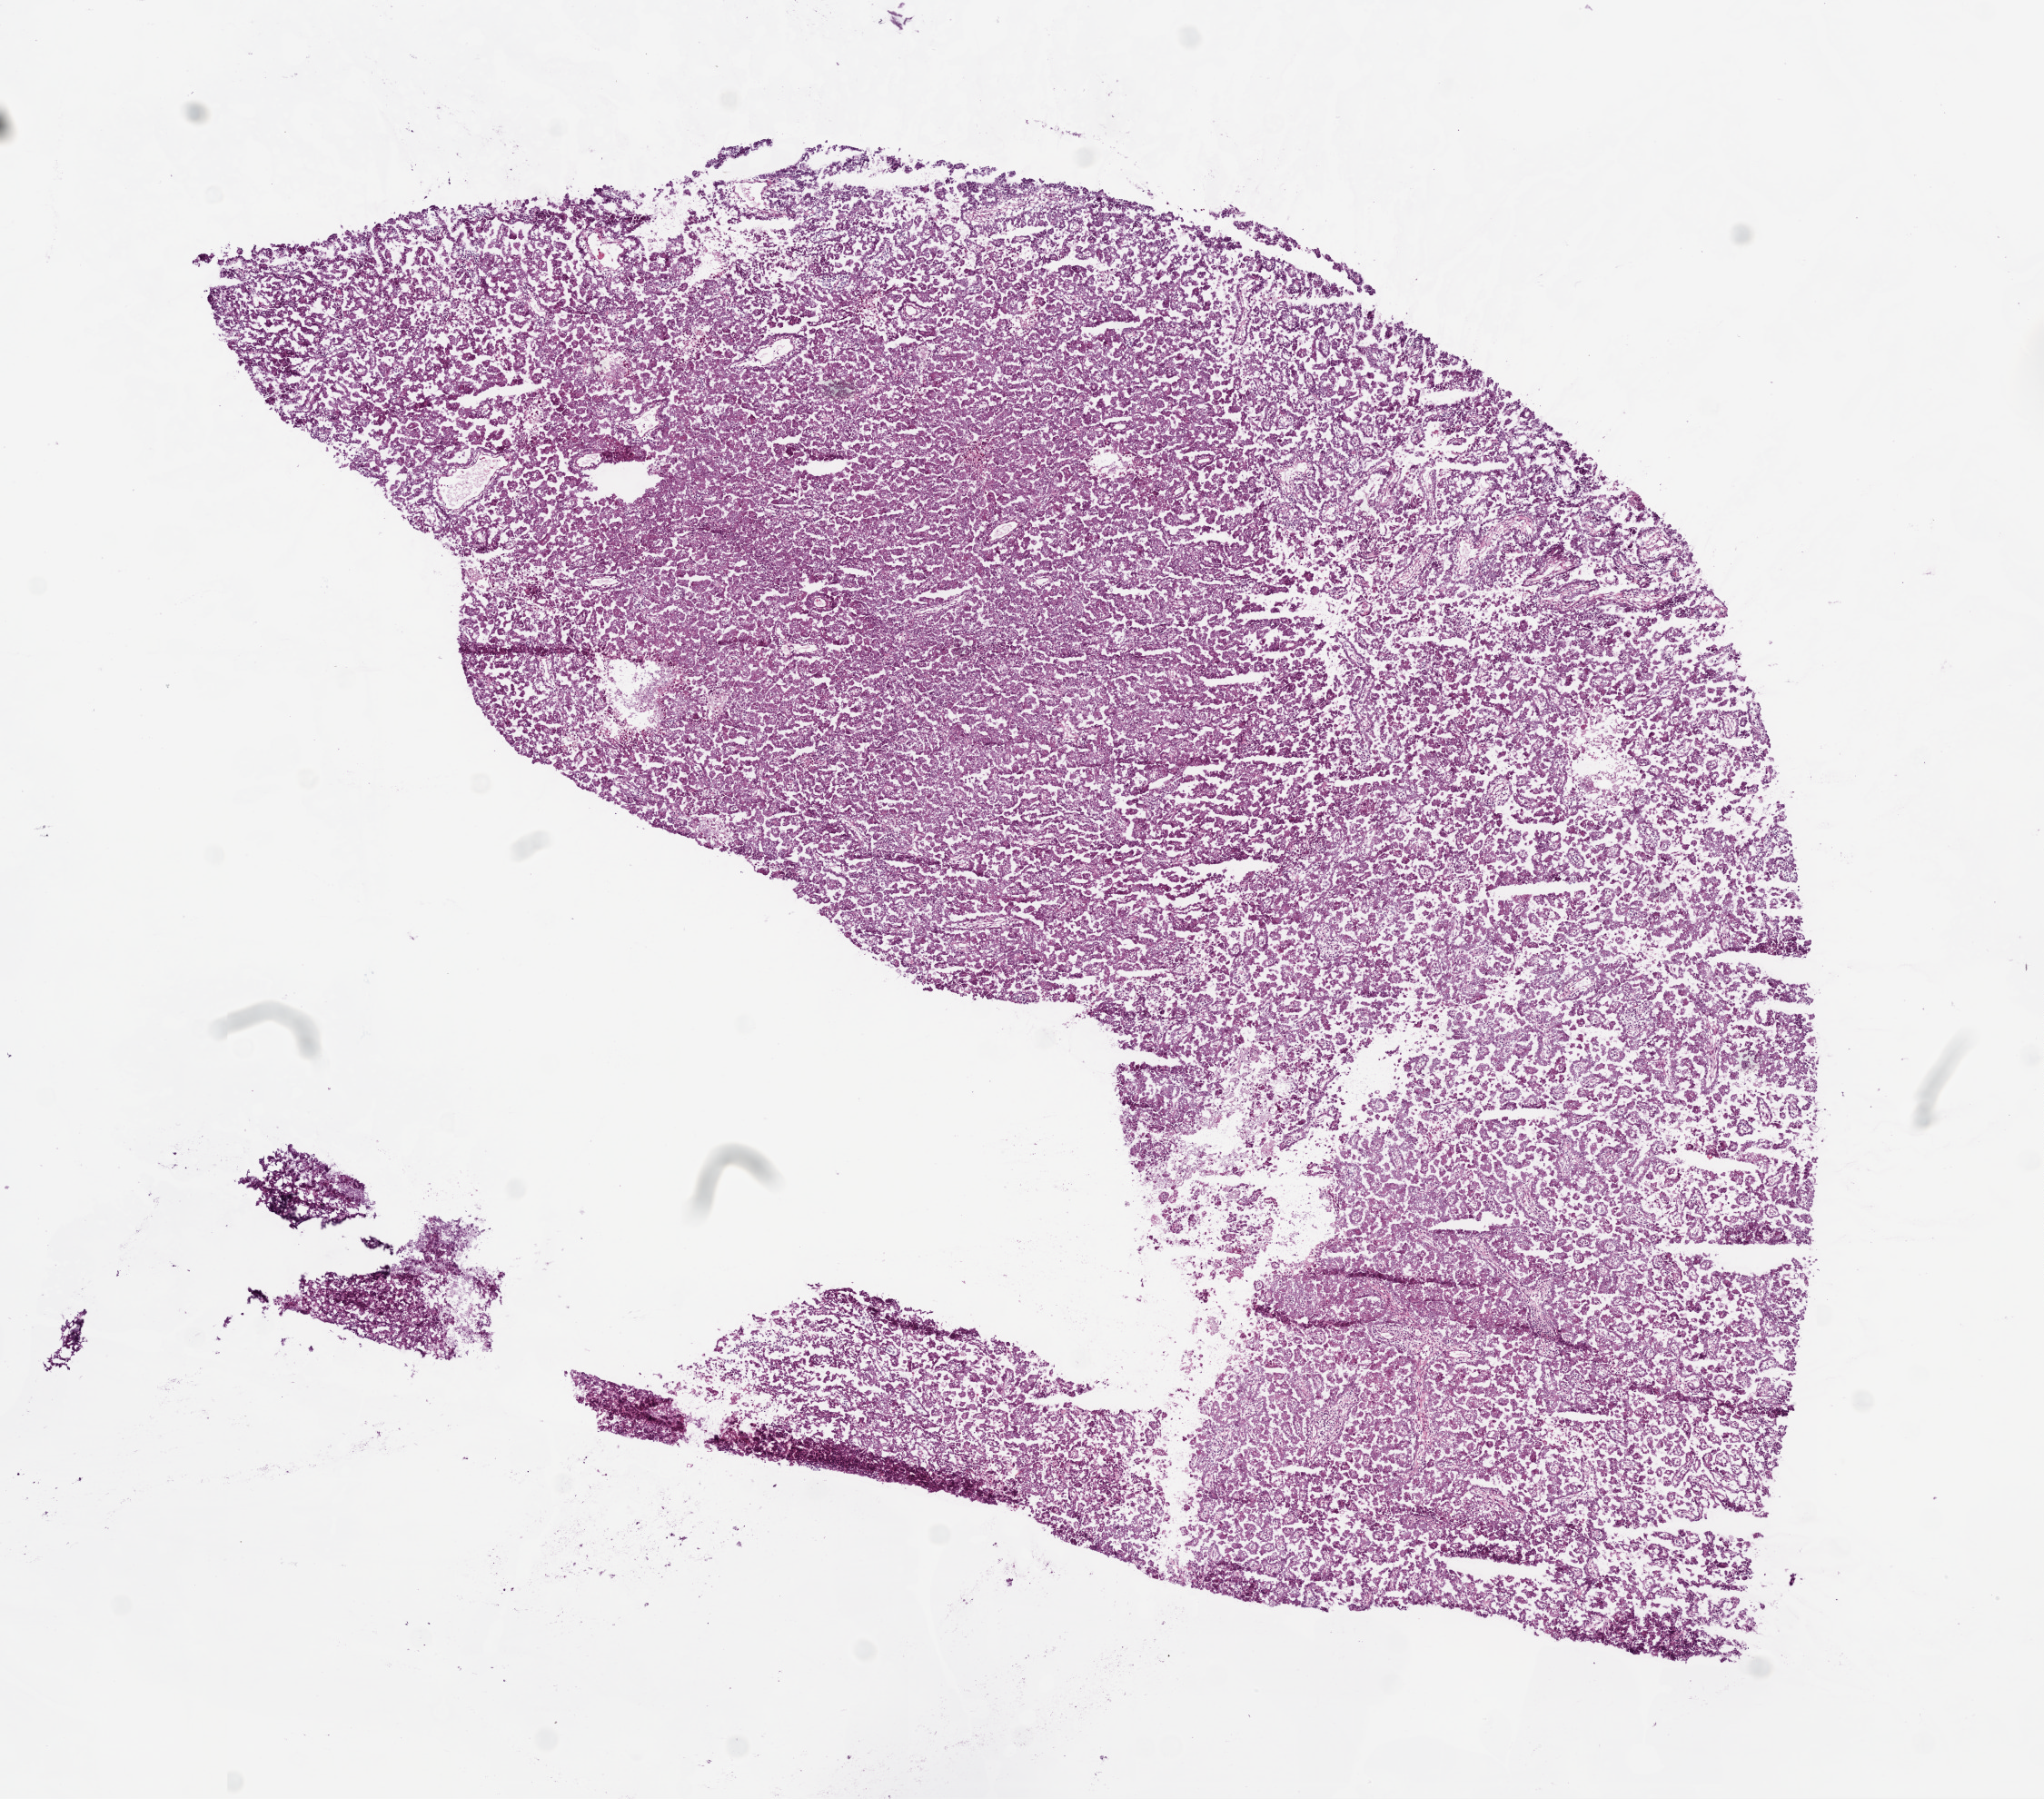
H&E-stained whole-slide image, whole scanned area (about 9.0 x 7.9 mm, acquisition: 20x scan) shown as a low-resolution overview, frozen section, kidney, primary tumour sample. Female, age 75 years at initial diagnosis. Pathologist review of this section (percent, as recorded): tumour cells 78%, tumour nuclei 85%.
Pathologic diagnosis: Papillary adenocarcinoma, NOS.